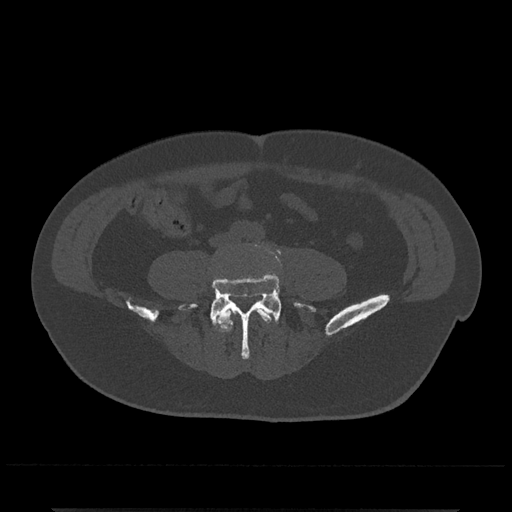
CT including the spine, one axial slice. Slice 107 of 797 in the series (ordered by position). Reconstruction kernel Br40s/3. 120 kVp. Bone window (W 1800 / L 400 HU). 0.5 mm slice thickness. 512 × 512 image matrix, field of view 393 × 393 mm. Patient: male, 67 years. Case-level facts recorded for this patient, not image findings: primary cancer: prostate.
Structures marked on this image (semi-automatic segmentation, software-assisted and operator-edited):
- L4 vertebra: bounding box (x1, y1, x2, y2) in pixels: (216, 302, 277, 332)
- L5 vertebra: (179, 244, 315, 359)